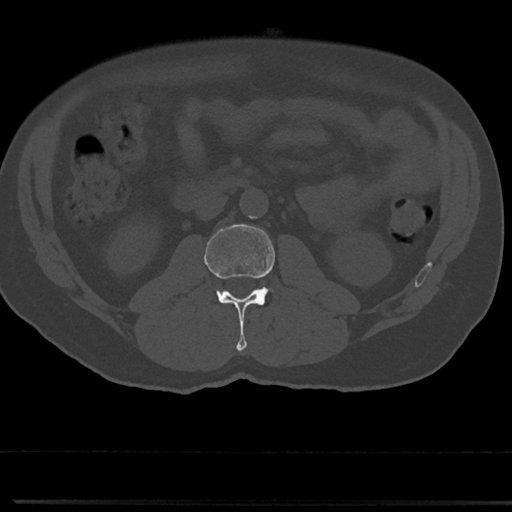
CT including the spine, one axial slice. Slice 5 of 817 in the series (ordered by position). Bone window (W 1800 / L 400 HU). 0.5 mm slice thickness. 512 × 512 image matrix. Male patient, age 61 years. Case-level facts recorded for this patient, not image findings: primary cancer: prostate.
Structures marked on this image (semi-automatic segmentation, software-assisted and operator-edited):
- L2 vertebra: bounding box [x1, y1, x2, y2] px = [205, 225, 280, 350]